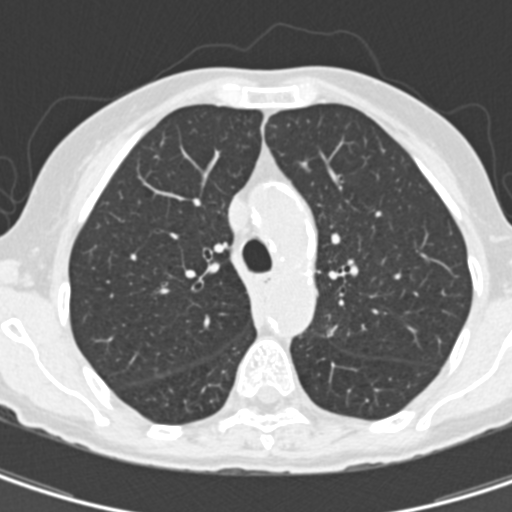
Low-dose screening chest CT, one axial slice. Slice 107 of 157 in the series (ordered by position). Reconstruction kernel B30f. Lung window (W 1500 / L -600 HU). 2 mm slice thickness. 512 × 512 image matrix, field of view 260 × 260 mm.
Annotated regions visible in this slice (expert manual segmentation):
- lesion 1 (tumor, upper lobe of left lung): bounding box [x1, y1, x2, y2] px = [327, 325, 338, 337]